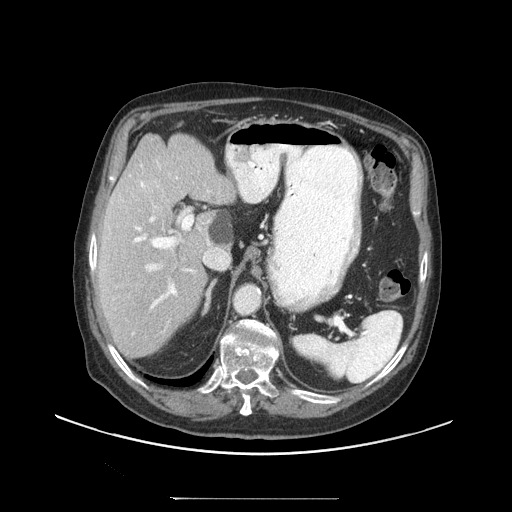
Contrast-enhanced abdominal CT (liver protocol), one axial slice. Slice 65 of 97 in the series (ordered by position). 140 kVp. Soft-tissue window (W 400 / L 40 HU). 512 × 512 image matrix, field of view 450 × 450 mm. Case-level facts recorded for this patient, not image findings: diagnosis: hepatocellular carcinoma (patient treated with transarterial chemoembolisation; whether this scan precedes or follows treatment is not stated here); TNM stage (as recorded): Stage-IIIC; Child-Pugh class: A; tumour differentiation: well differentiated; tumour nodularity: uninodular.
Outlined on this slice (semi-automatically segmented with operator editing):
- liver parenchyma outside the tumour (the mass and vessels are separate outlines, so this box may not span the whole liver): bounding box (x1, y1, x2, y2) in pixels: (96, 134, 236, 358)
- liver vessels: (134, 161, 210, 308)